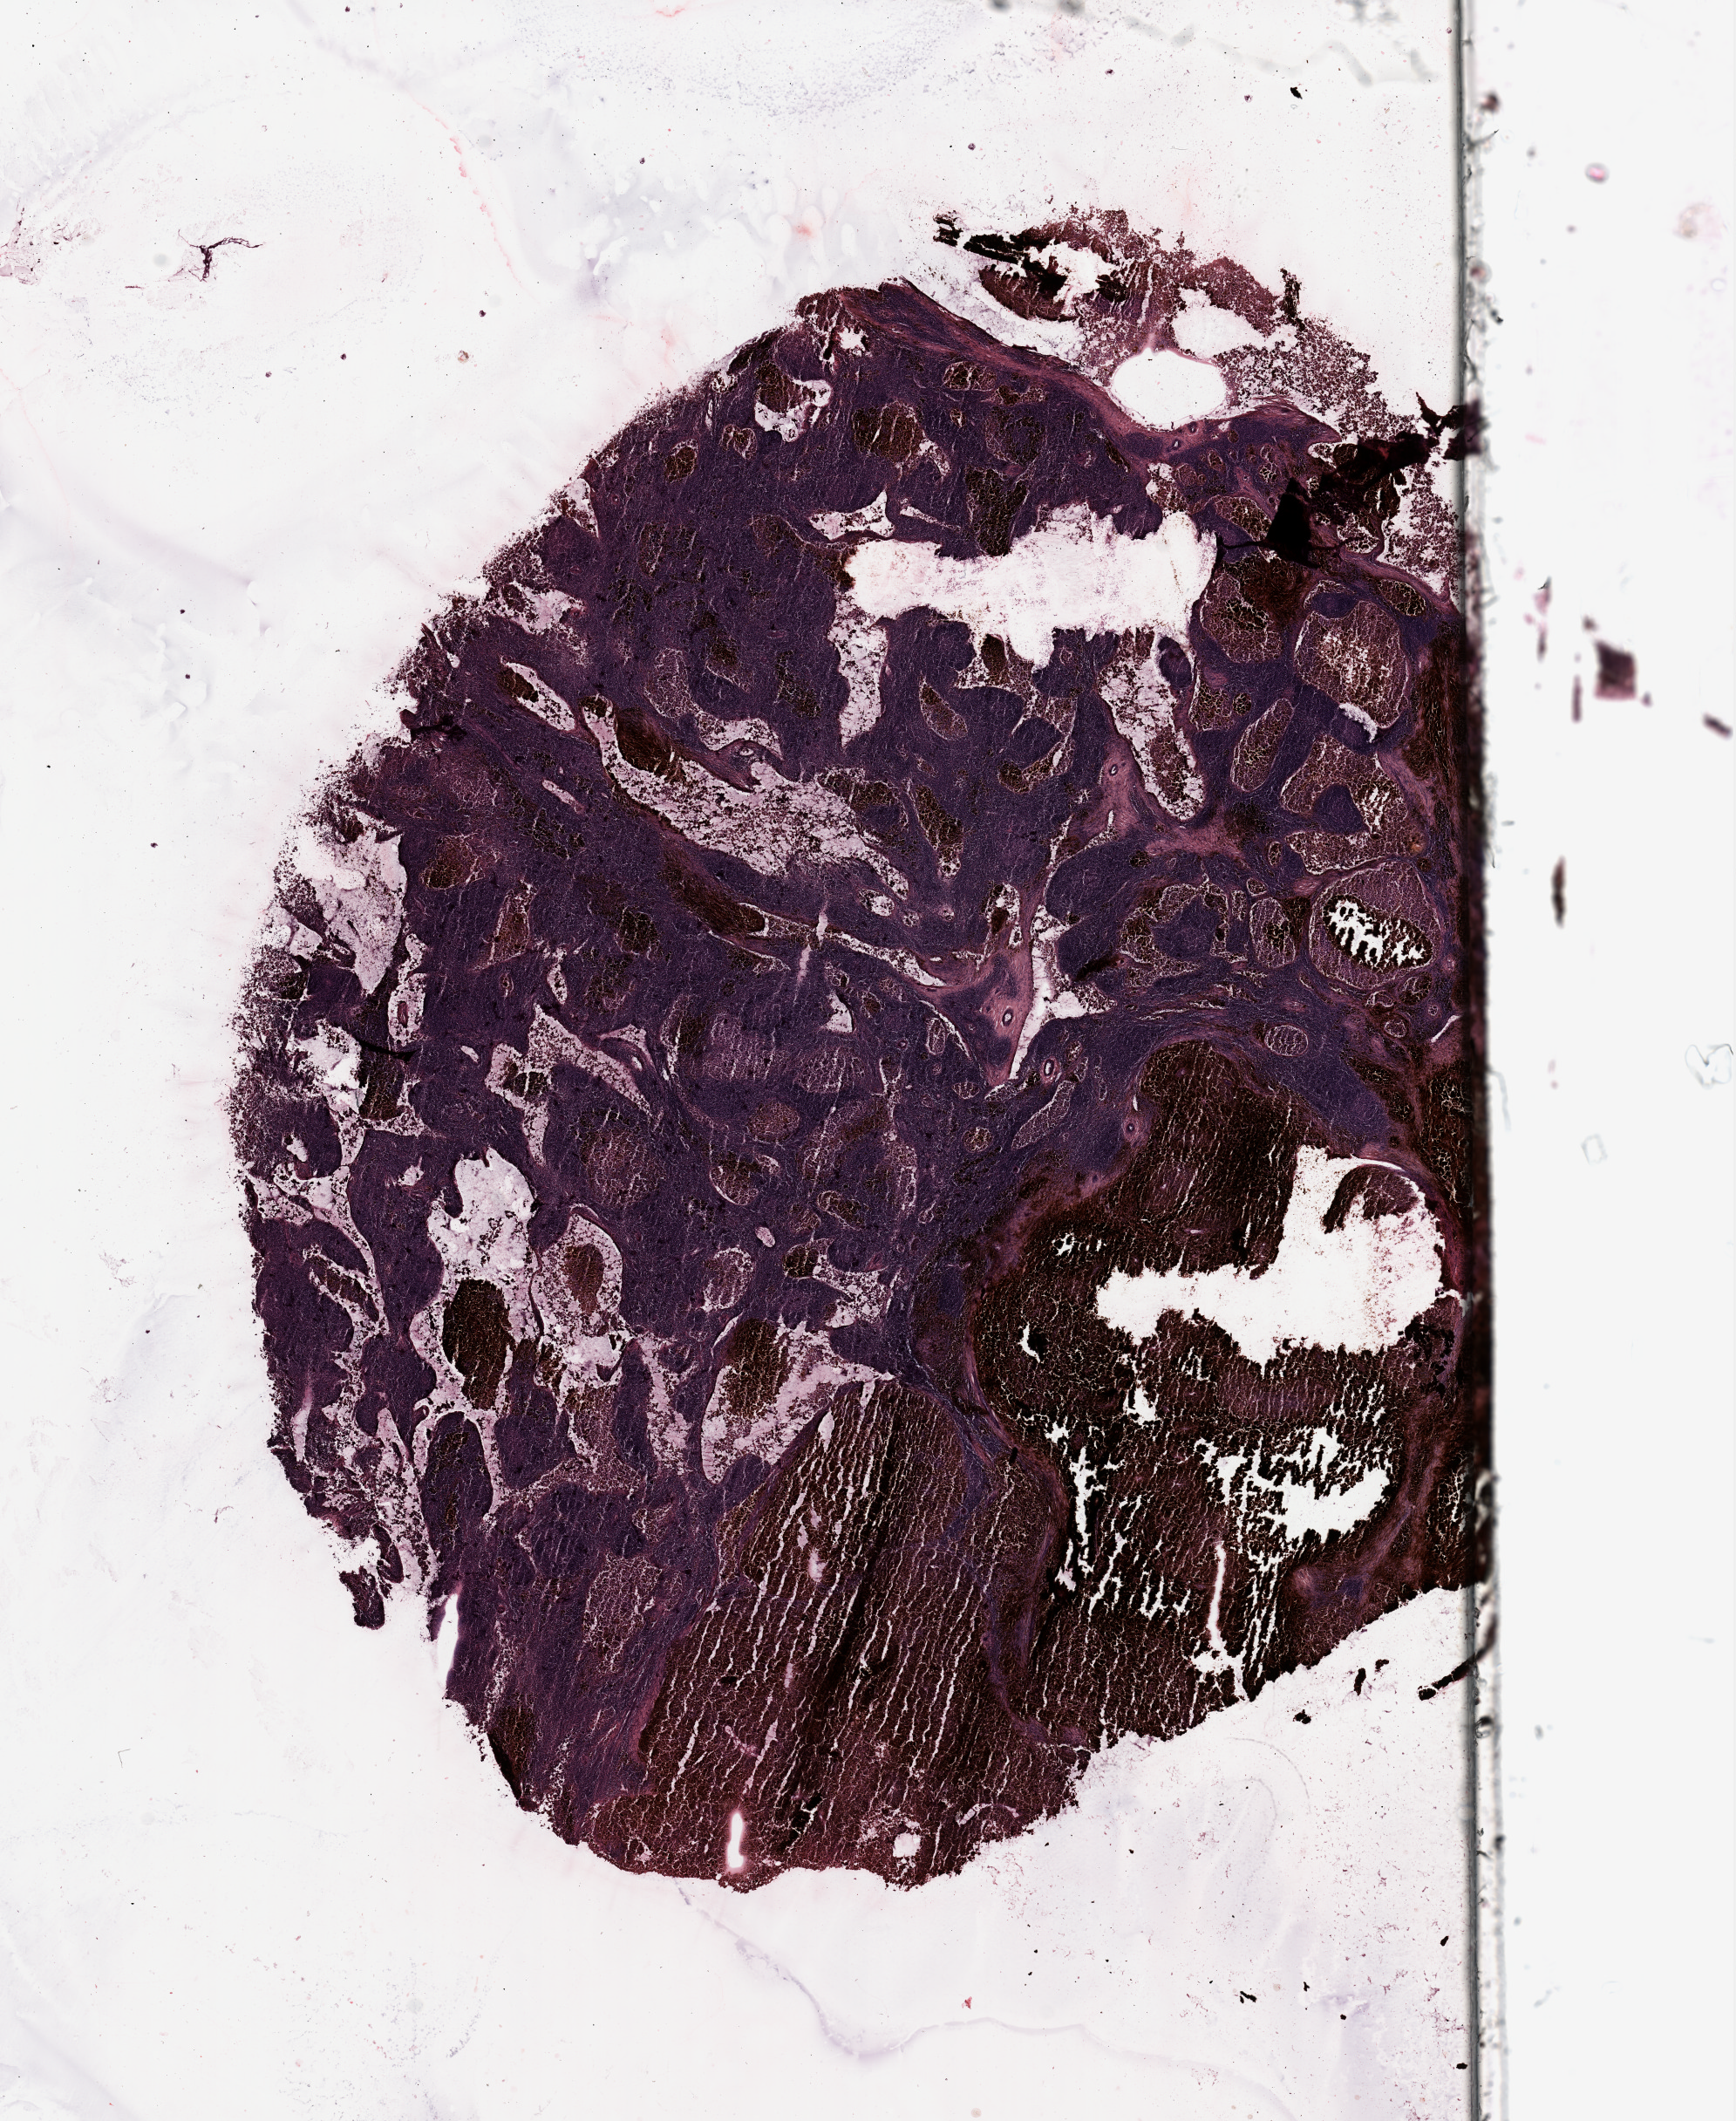
Digitized H&E-stained tissue section (whole slide), whole scanned area (about 15.8 x 19.2 mm, acquisition: 20x scan) shown as a low-resolution overview. Melanoma tumour tissue; sampled site not recorded. Female, 23 y/o.
Patient diagnosis (cohort enrolment): cutaneous melanoma (skin).